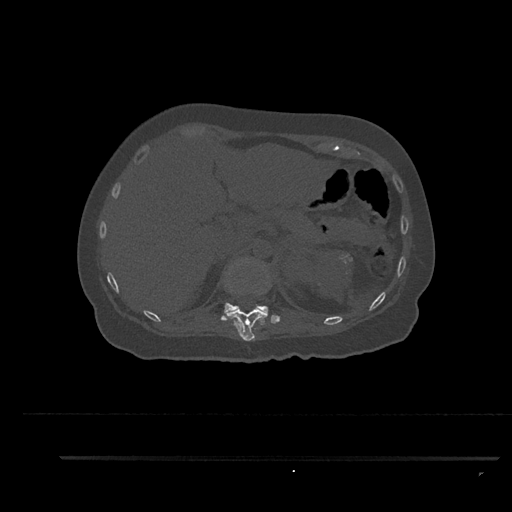
CT including the spine, one axial slice; position 293 of 797 along the scan axis; 120 kVp; bone window (W 1800 / L 400 HU); 0.5 mm slice thickness; 512 × 512 image matrix, field of view 408 × 408 mm. Female patient, age 44 years. Case-level facts recorded for this patient, not image findings: primary cancer: renal; vertebrae with lytic lesions (as recorded): L1.
Structures marked on this image (semi-automatically segmented with operator editing):
- T11 vertebra: bounding box <230,292,268,341> (left, top, right, bottom; pixels)
- T12 vertebra: <220,259,280,321>